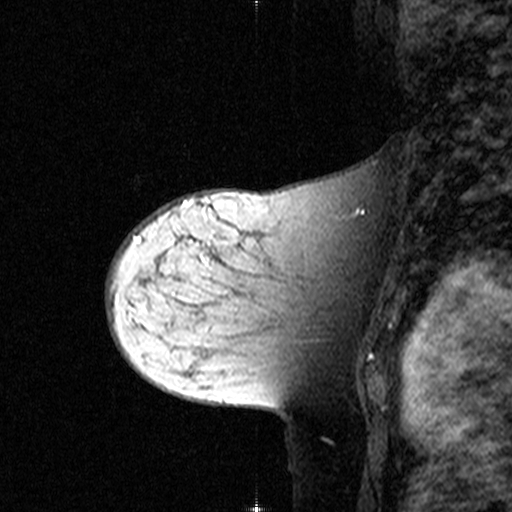
Breast MRI (dynamic contrast-enhanced), one sagittal slice. Slice 29 of 44 in the series (ordered by position). Dynamic contrast-enhanced study with each time point stored as its own series, time point 2 of 3 at this slice position (early post-contrast, ordered by acquisition time). 1.5 T. TE 4.5 ms, TR 11 ms. 512 × 512 image matrix, field of view 200 × 200 mm. Female patient, age 44 years. Case-level facts recorded for this patient, not image findings: setting: breast cancer imaged before/during neoadjuvant chemotherapy; receptor status: triple-negative.
Structures marked on this image (semi-automatic segmentation, software-assisted and operator-edited):
- analysis volume of interest (the breast-tissue region the enhancement analysis was run in; not a lesion): bounding box <142,208,349,363> (left, top, right, bottom; pixels)
- tumour enhancement mask (voxels above the 90 % enhancement threshold inside the analysis volume of interest): <202,242,210,253>